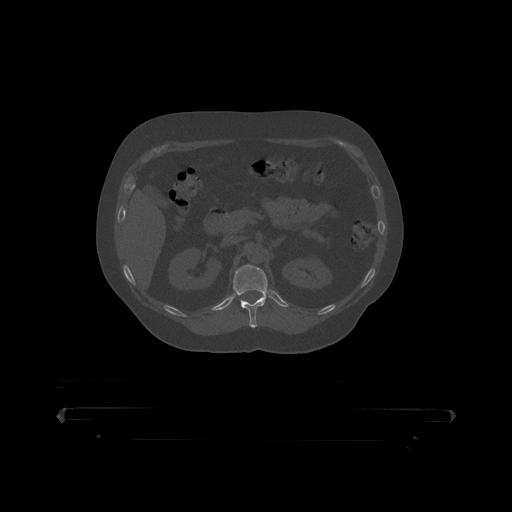
CT including the spine, one axial slice; position 167 of 390 along the scan axis; reconstruction kernel STANDARD; 120 kVp; bone window (W 1800 / L 400 HU); 1.25 mm slice thickness; 512 × 512 image matrix, field of view 650 × 650 mm. Male patient, age 60 years. Case-level facts recorded for this patient, not image findings: primary cancer: prostate.
Annotated regions visible in this slice (semi-automatically segmented with operator editing):
- T12 vertebra: bounding box <233,265,268,319> (left, top, right, bottom; pixels)